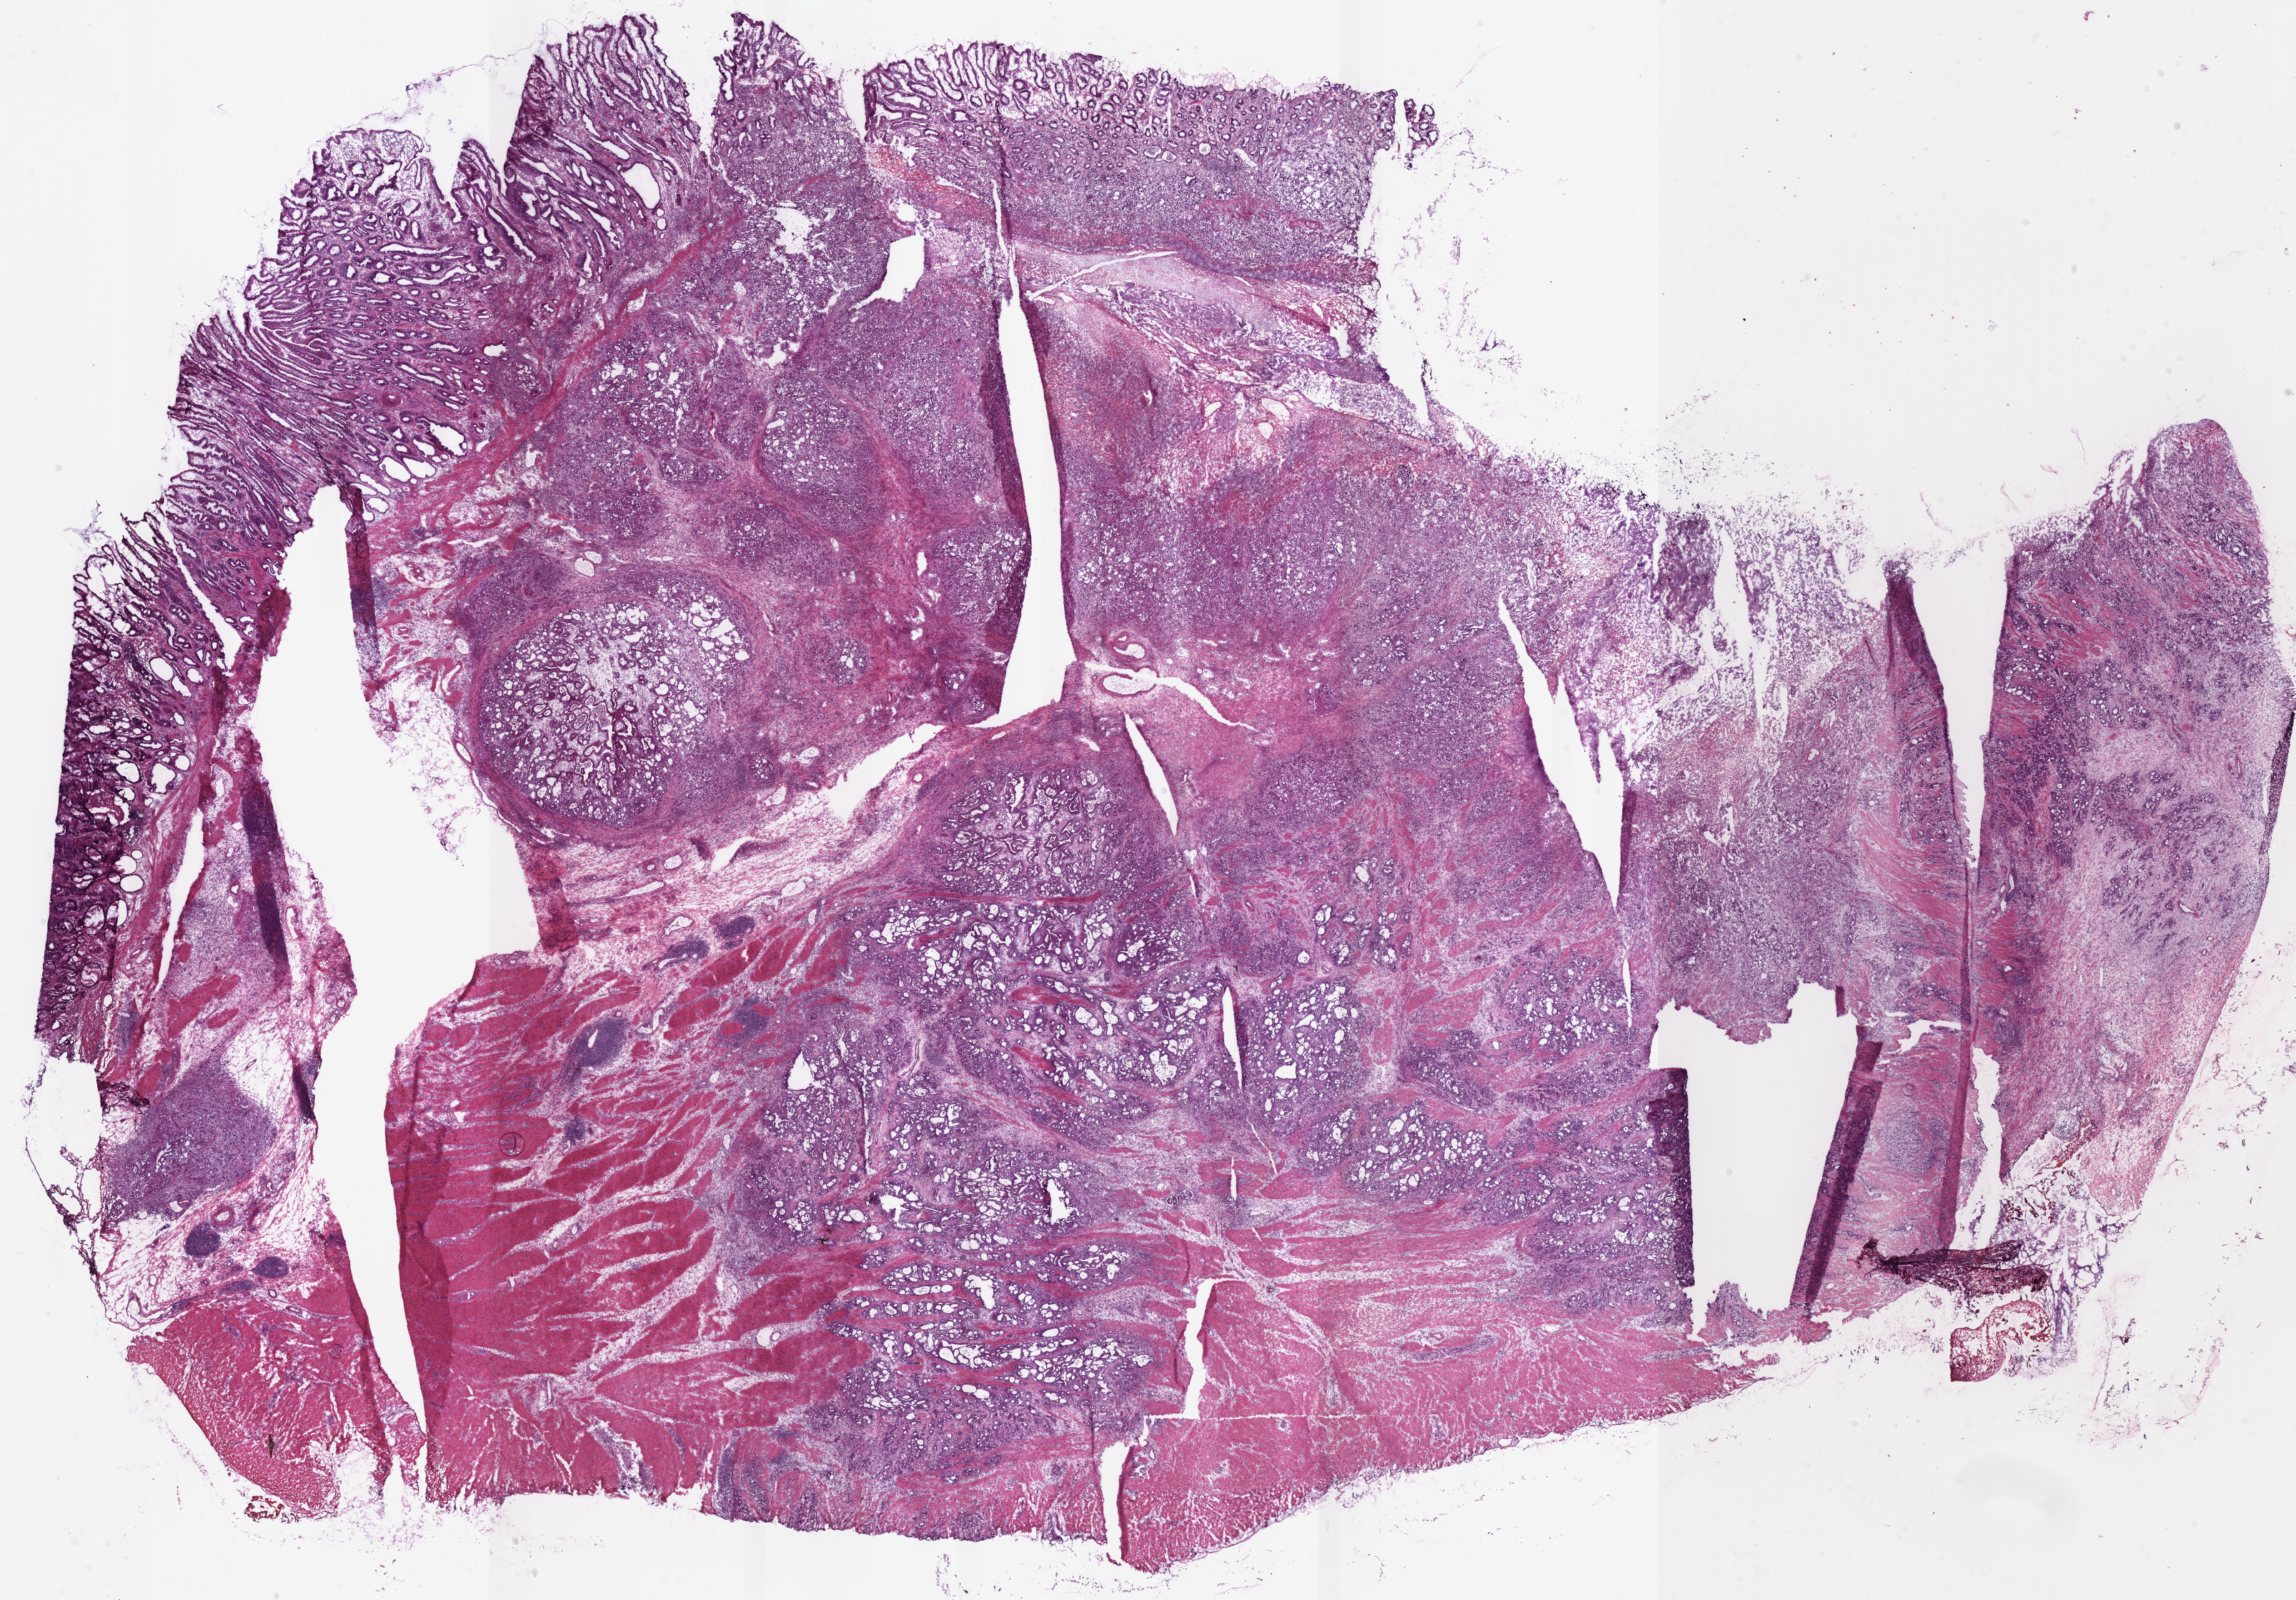
Hematoxylin and eosin (H&E) stained whole-slide image — low-resolution overview of the scanned area, about 25.3 x 17.6 mm; frozen section from the bottom of the tissue portion; sample: primary tumour, stomach. Patient: male, age at initial diagnosis 75 years. Histologic grade: G3 (poorly differentiated). Composition of this section per pathologist review: tumour cells 71%, tumour nuclei 65%, normal cells 14%, stromal cells 11%, necrosis 4%. Infiltration values recorded for this section: lymphocyte infiltration 10%, monocyte infiltration 10%, neutrophil infiltration 5%.
Diagnosis: Tubular adenocarcinoma (gastric antrum). AJCC pathologic stage: IIIB.